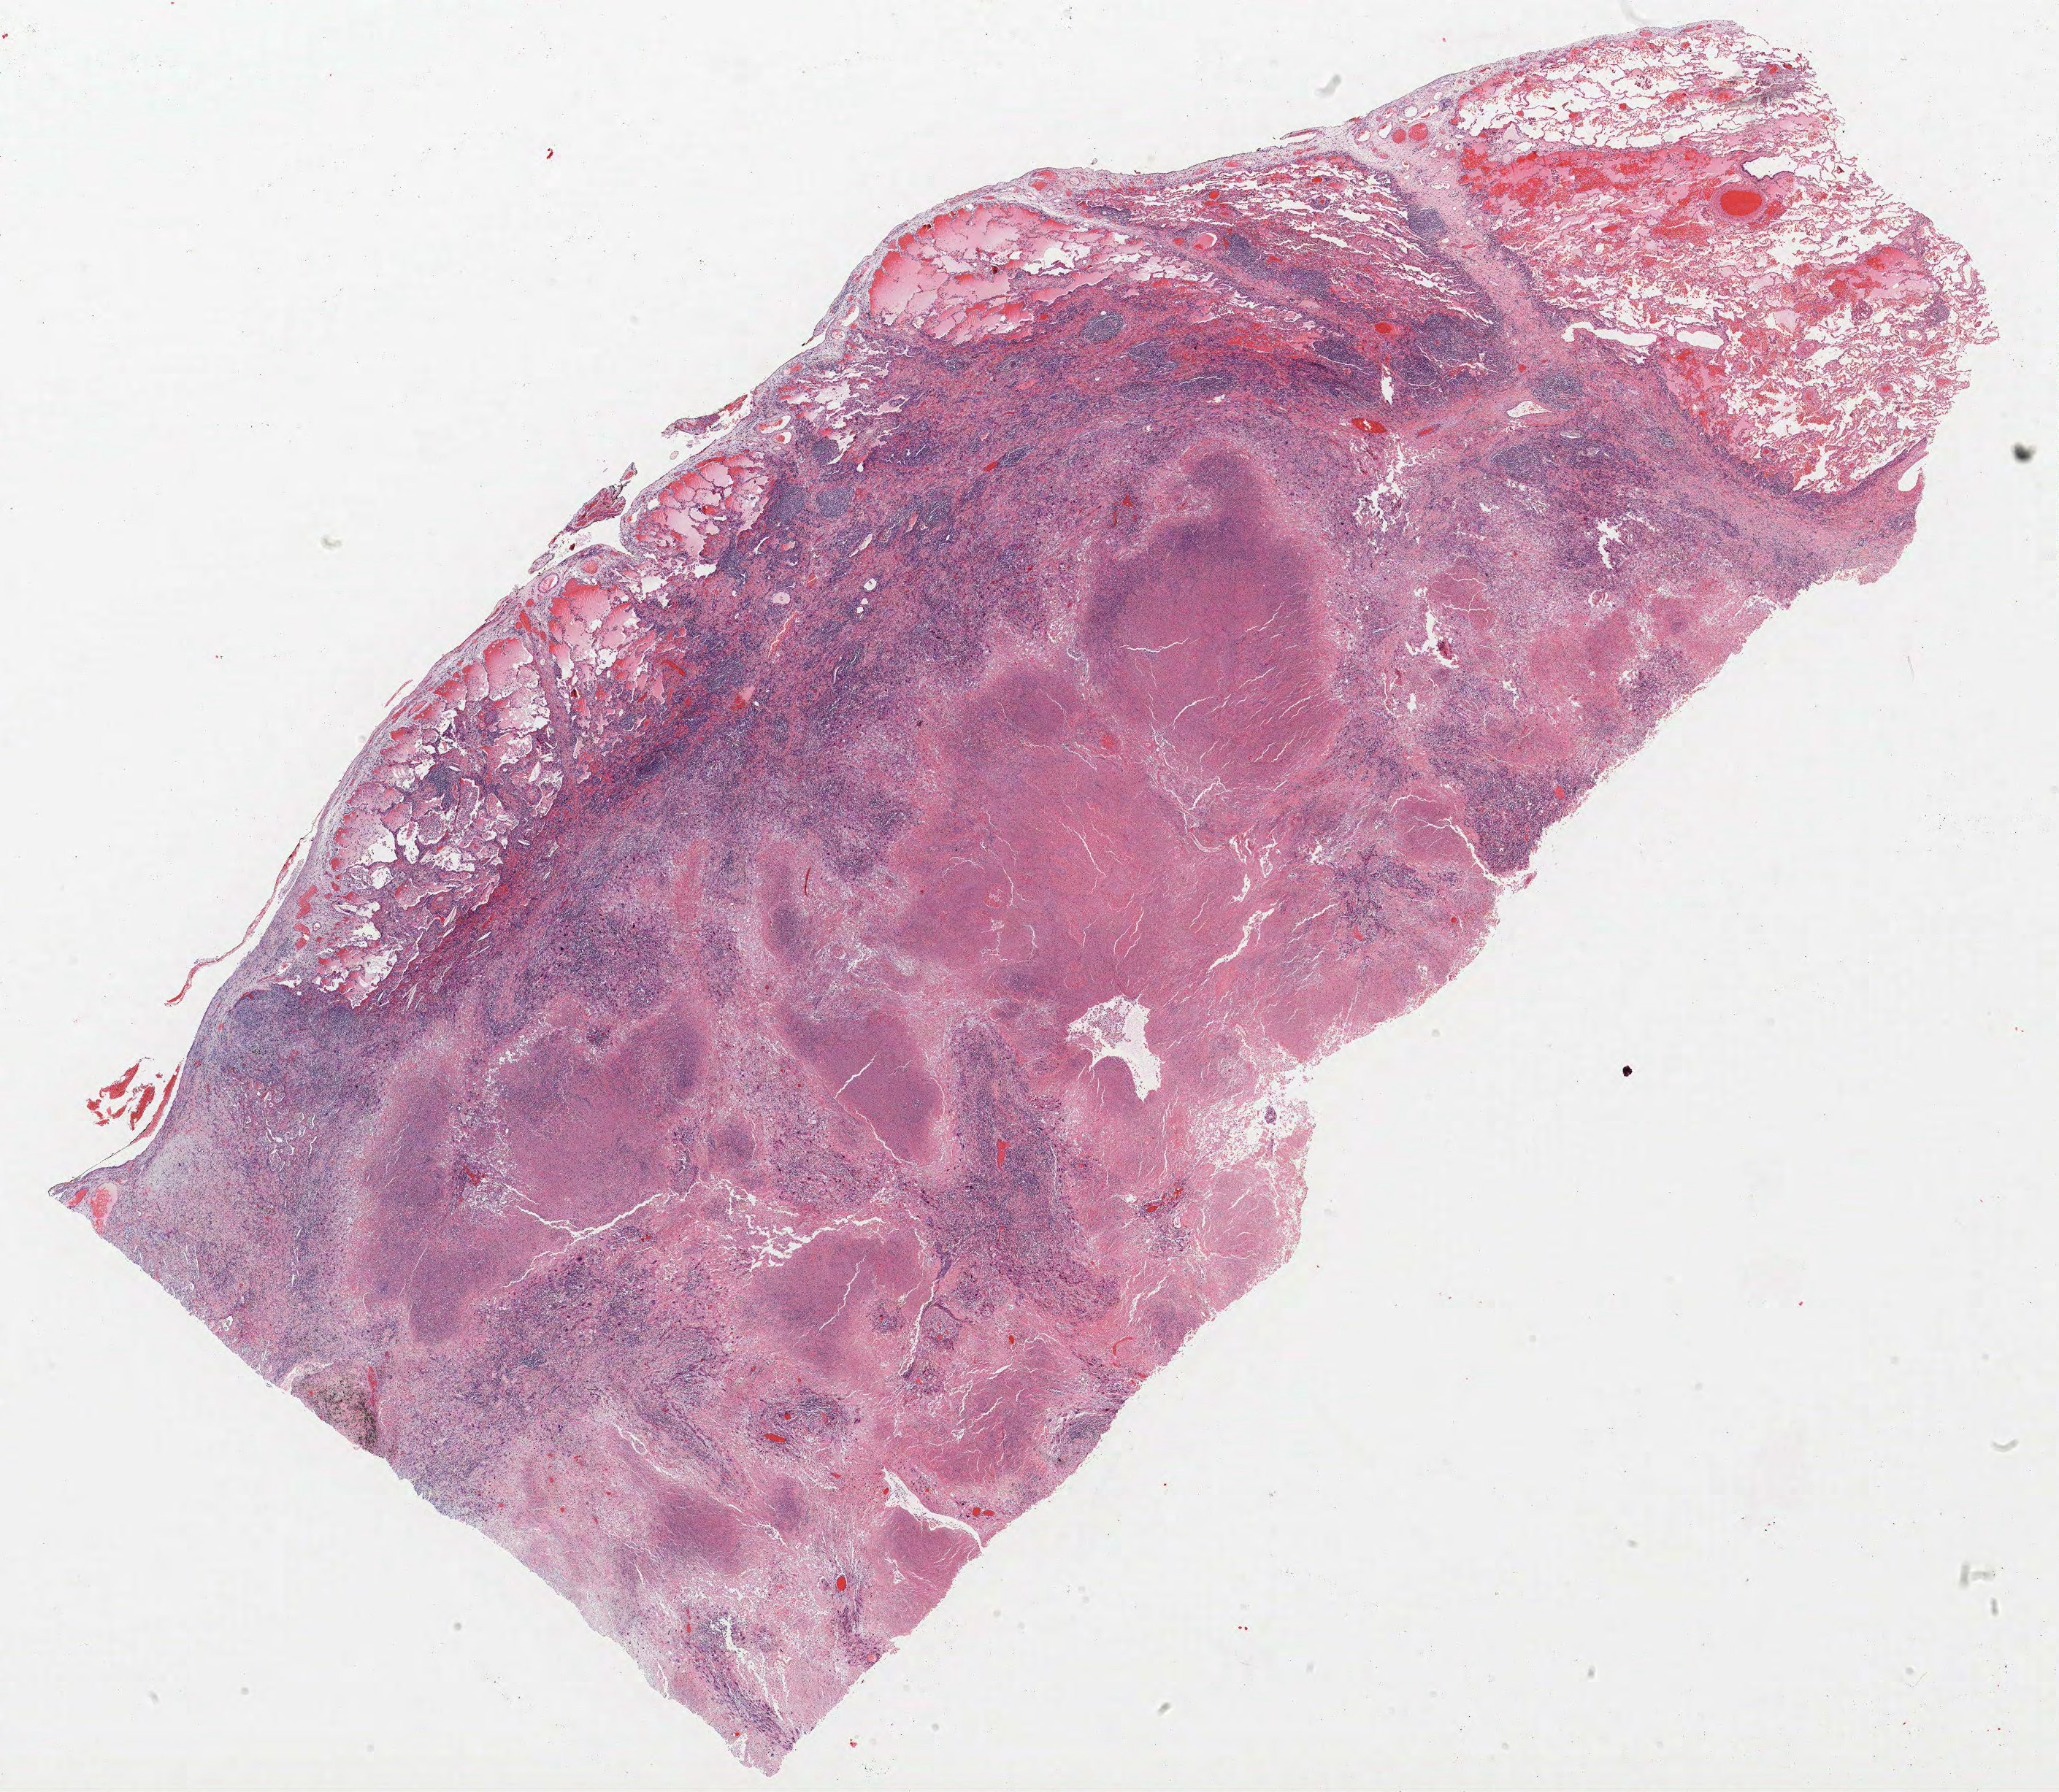
Whole-slide histology image, H&E, a low-resolution overview of the entire scanned area, about 22.6 x 19.6 mm. Formalin-fixed paraffin-embedded (FFPE) section. Lung tissue. Male patient, aged 72 at enrolment. Former smoker at enrolment.
Participant's lung-cancer diagnosis: Squamous cell carcinoma, NOS (ICD-O-3 8070/3).